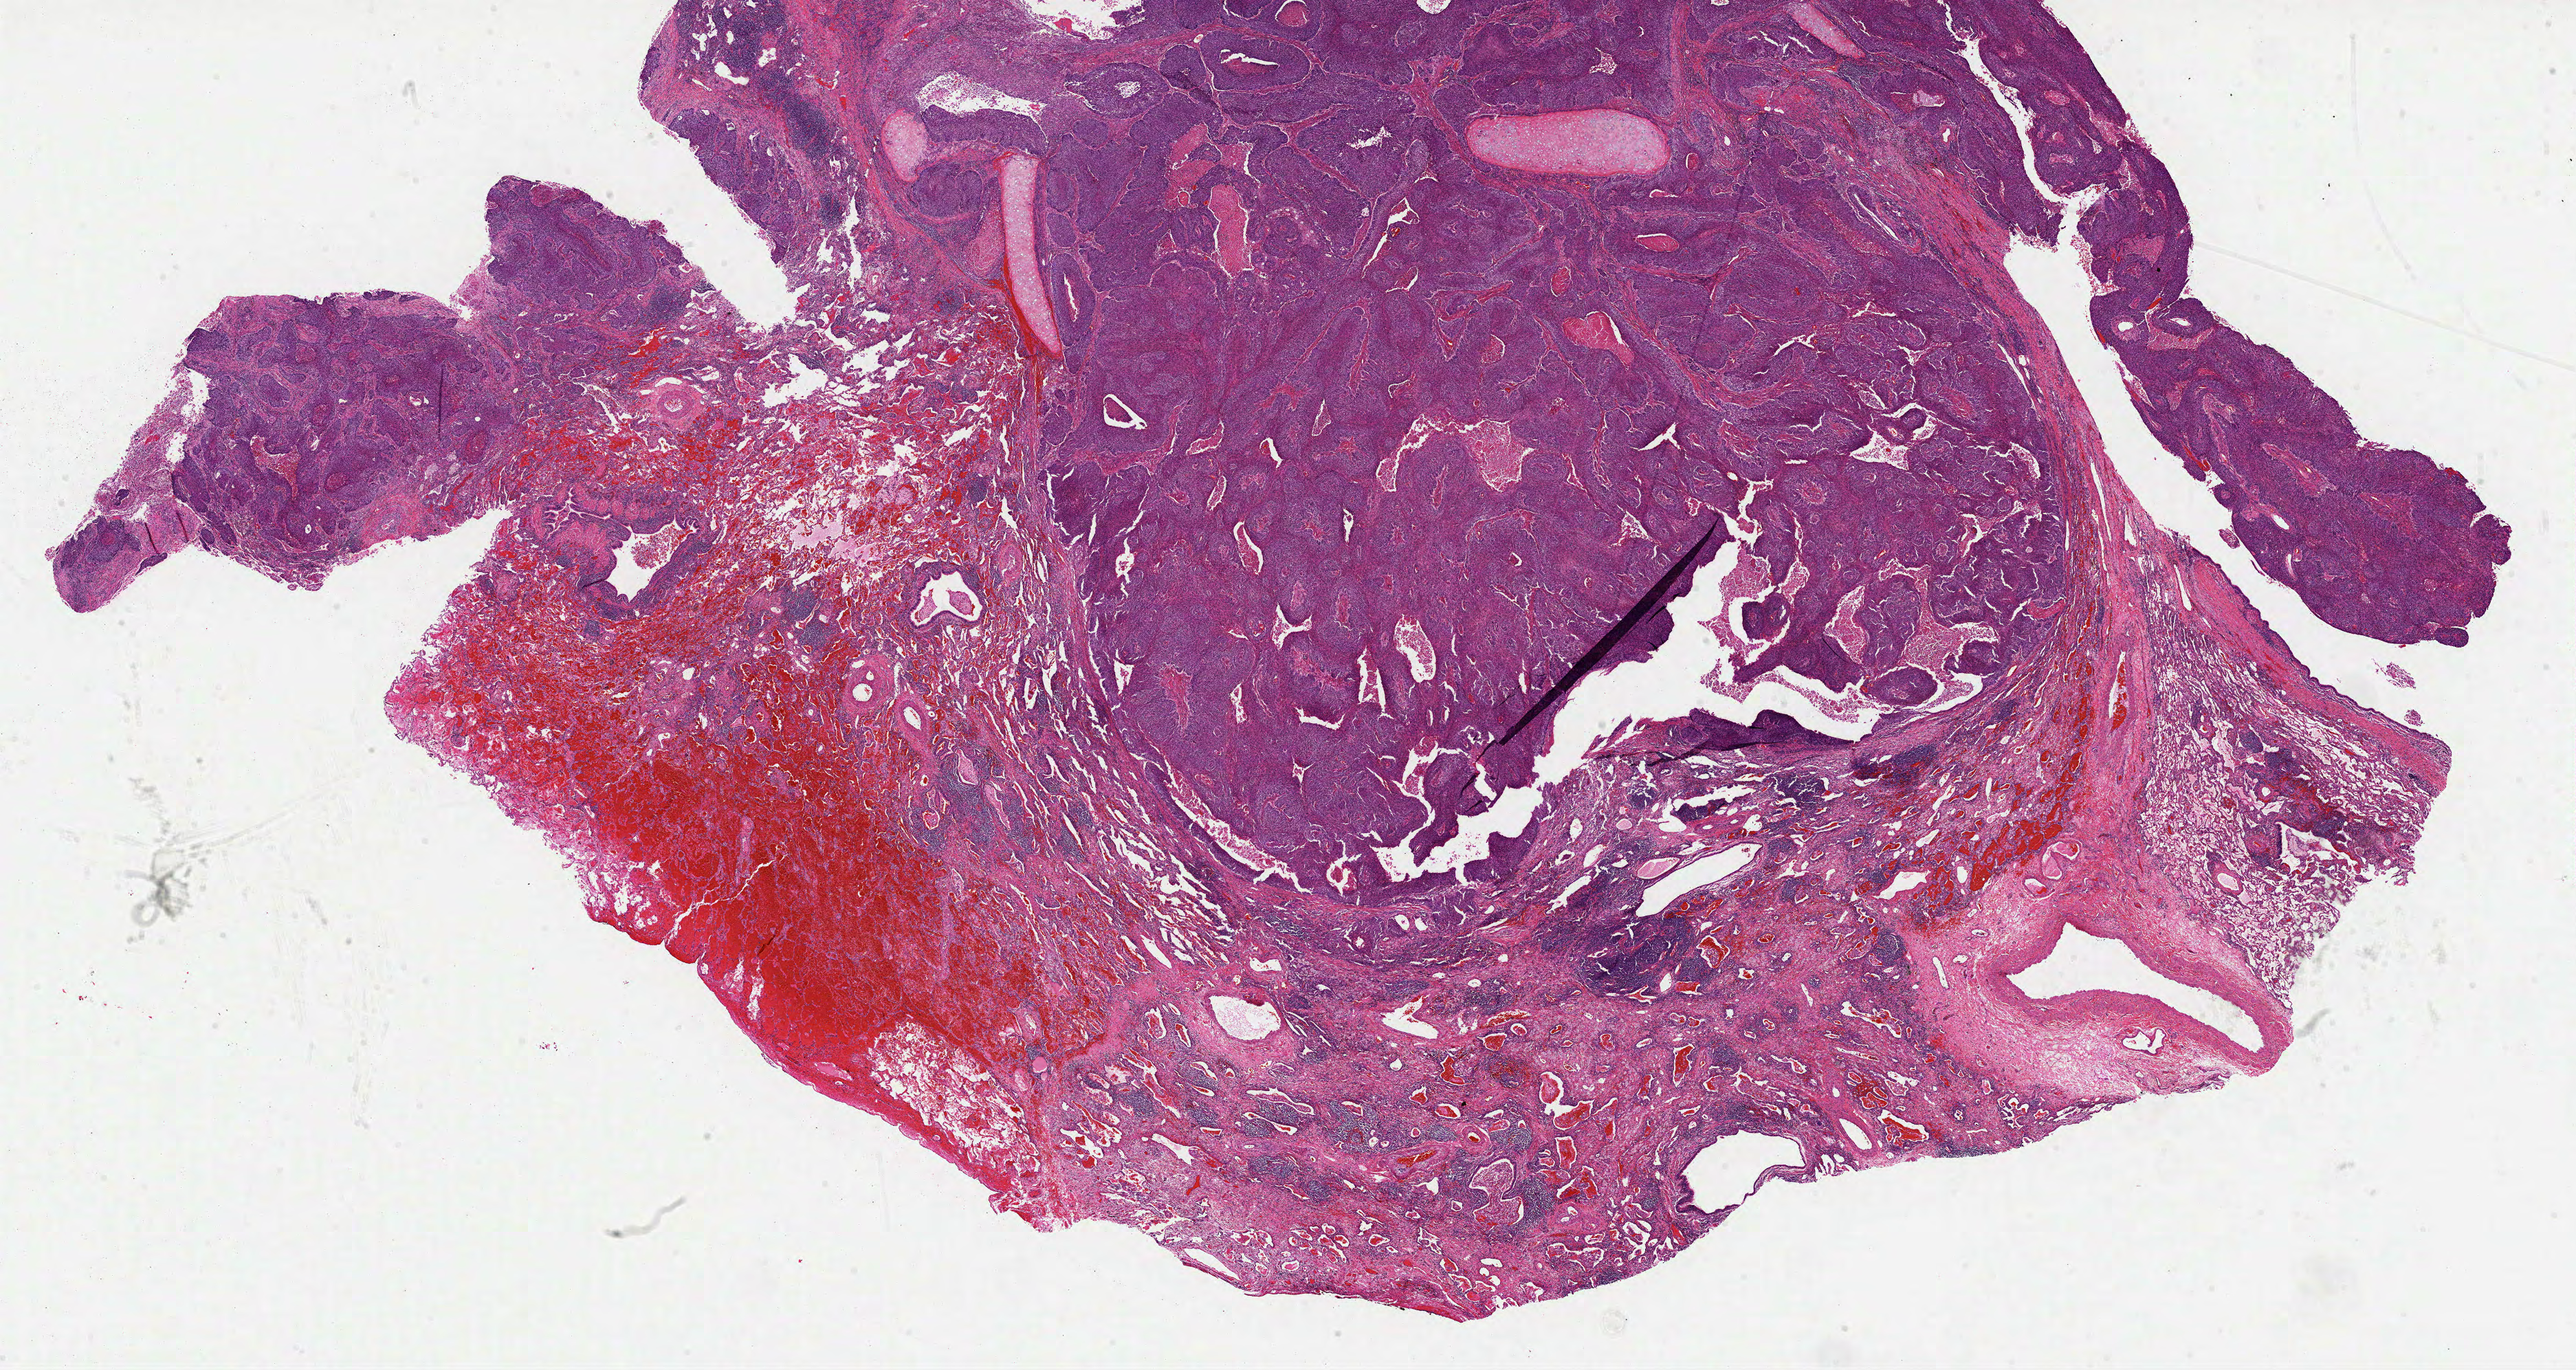
Whole-slide histology image, H&E-stained — whole scanned area (about 30.2 x 16.1 mm, from a 40x scan) shown as a low-resolution overview. Formalin-fixed paraffin-embedded (FFPE) diagnostic section. Primary tumour sample from the lung. Patient: male, age at initial diagnosis 66 years.
AJCC pathologic stage: IIIA (6th edition). Laterality: left. Histologic diagnosis: Squamous cell carcinoma, NOS (upper lobe, lung).